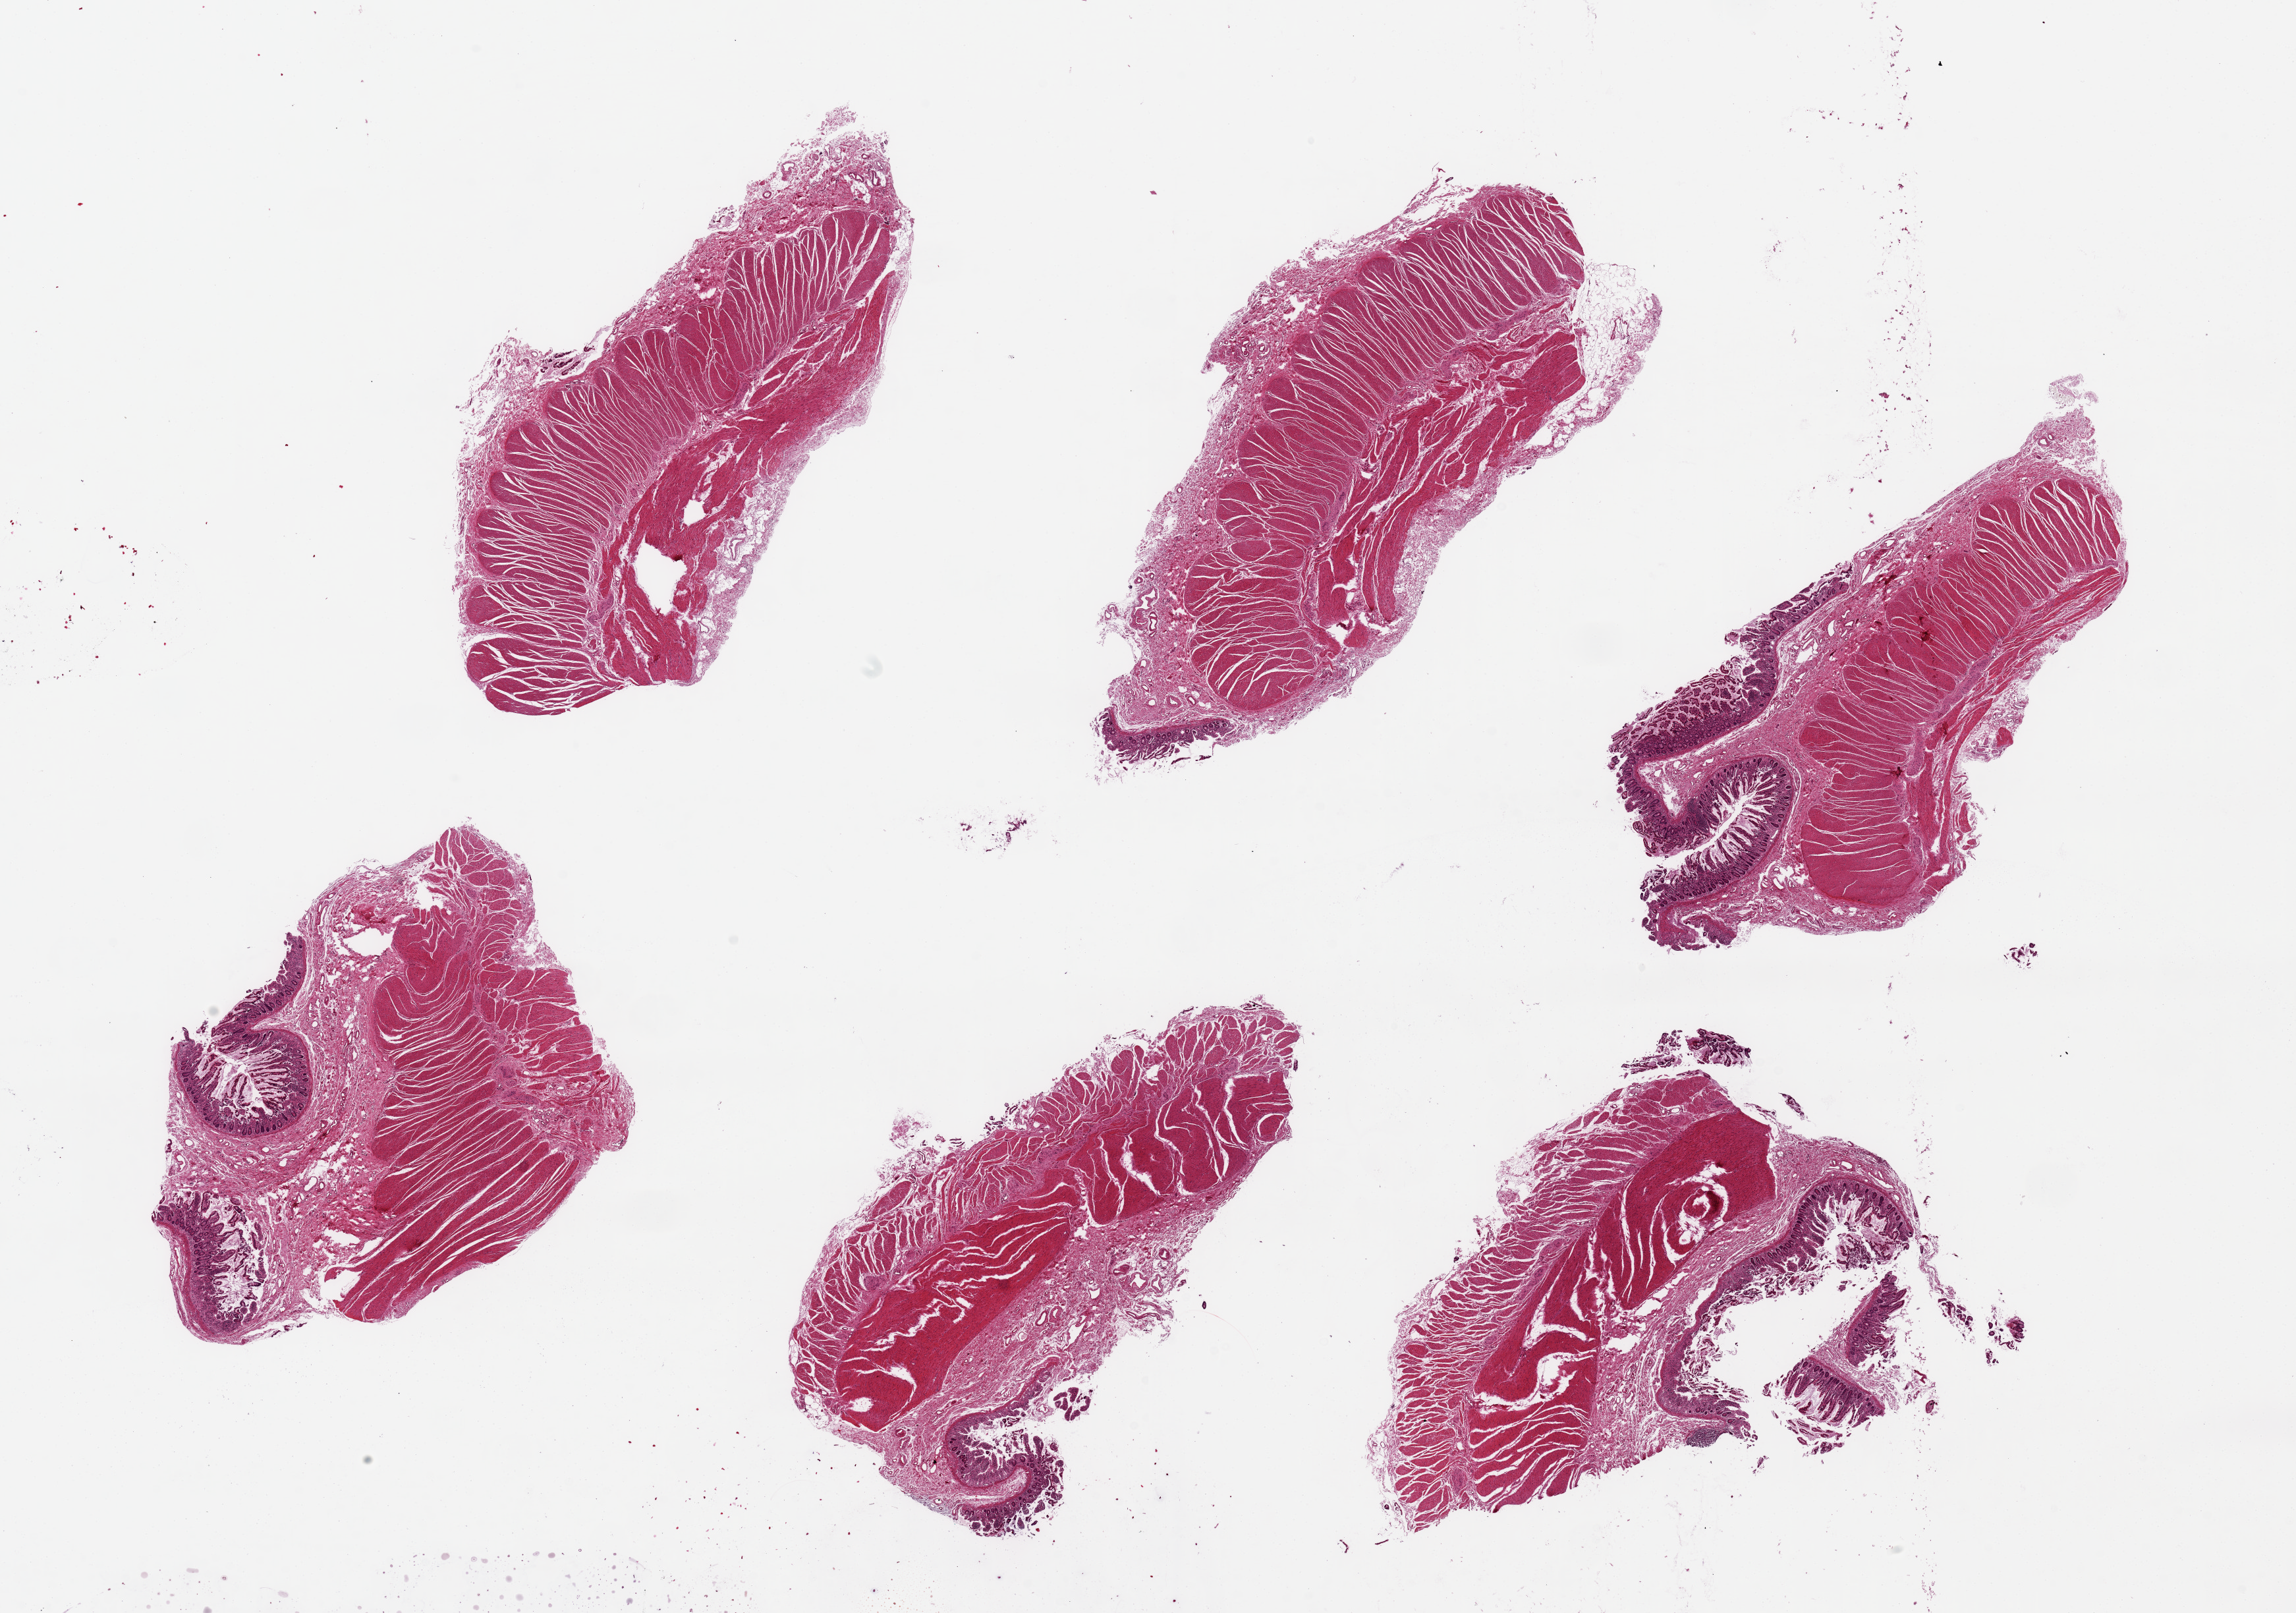
Digitized hematoxylin and eosin (H&E)-stained section — whole scanned area (about 27.6 x 19.4 mm) shown as a low-resolution overview, PAXgene-fixed paraffin-embedded (PFPE) section, sampled site (target tissue): ileum, donor tissue sample. Female donor.
Review note (as recorded): 6 pieces ~8x3mm, <10 % muscoa, no Peyer patches, mainly muscle.